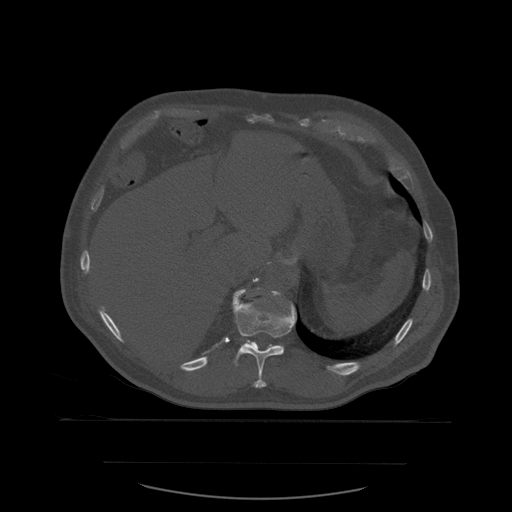
CT including the spine, one axial slice; slice 292 of 590 in the series (ordered by position); bone window (W 1800 / L 400 HU); 512 × 512 image matrix. Patient age 71 years. Case-level facts recorded for this patient, not image findings: primary cancer: lung; vertebrae with lytic lesions (as recorded): T1, T2, L5, S1.
Annotated regions visible in this slice (semi-automatically segmented with operator editing):
- T11 vertebra: bounding box [x1, y1, x2, y2] px = [232, 289, 297, 388]
- T12 vertebra: [233, 288, 283, 346]